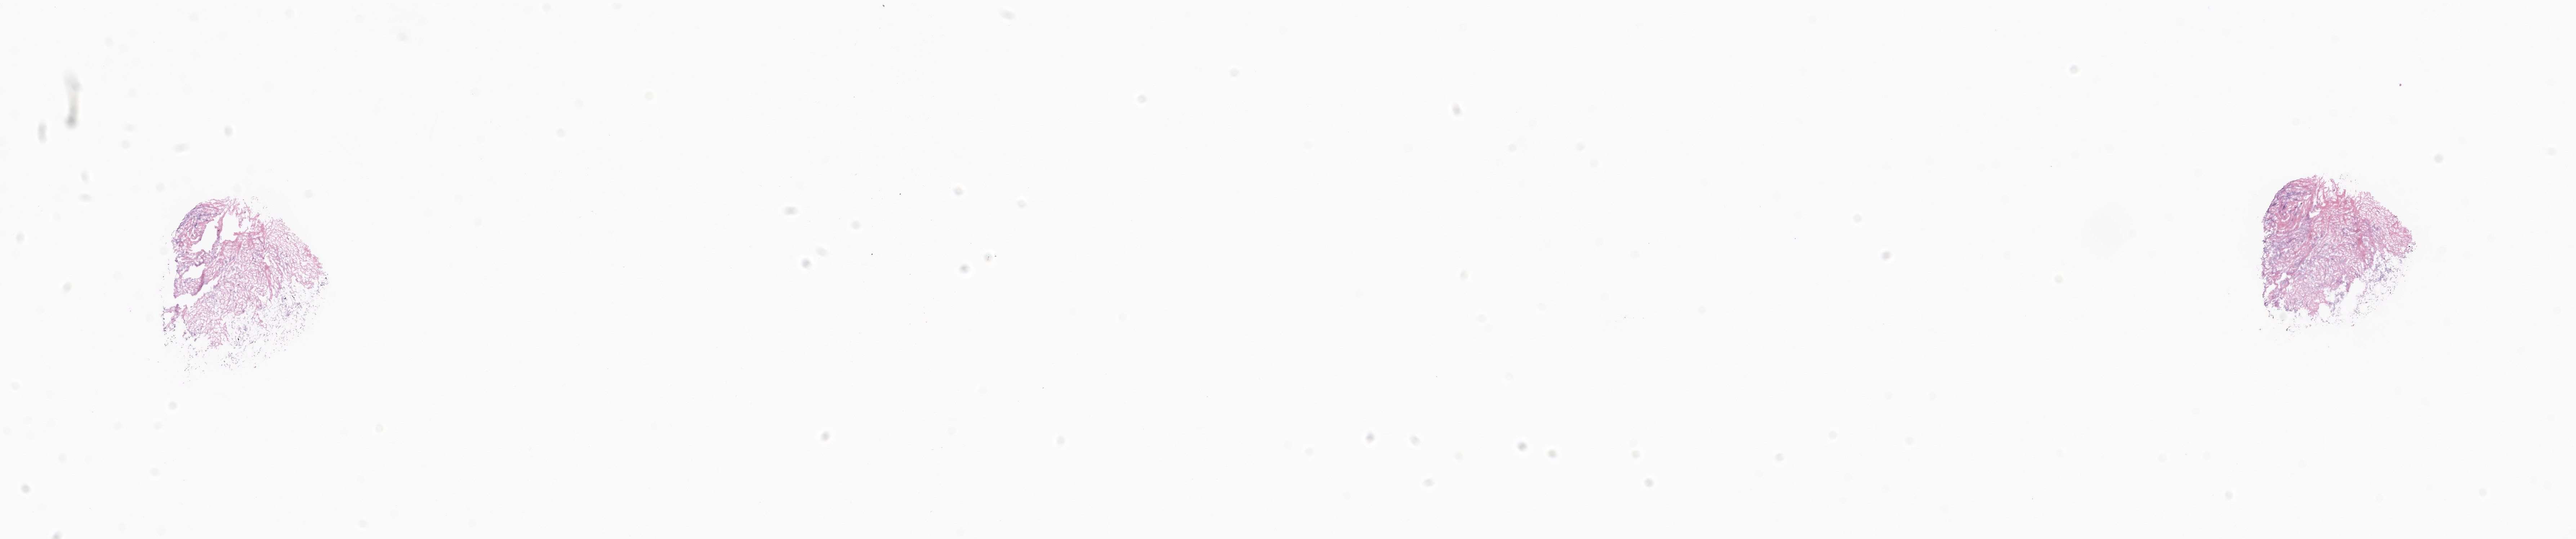
Whole-slide image, haematoxylin and eosin stain — whole scanned area (about 30.1 x 6.3 mm) shown as a low-resolution overview; frozen section; primary tumor; site: breast (right). Female, age 89 years at initial diagnosis. Pathologist review of this section (percent, as recorded): tumor cells 34%, tumor nuclei 85%, stromal cells 60%, necrosis 0%, normal cells 6%. Infiltration values recorded for this section: lymphocyte infiltration 0%, monocyte infiltration 0%, neutrophil infiltration 0%.
Diagnosis: Infiltrating duct carcinoma, NOS.